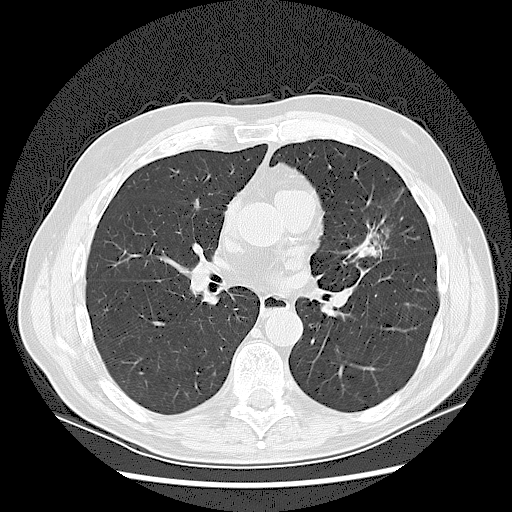
Low-dose screening chest CT, axial slice, baseline screening round, lung window (W 1500 / L -600 HU), lung (sharp) reconstruction kernel (LUNG), slice 65 of 132 in the series. Male participant, aged 65 years at enrolment. Current smoker at enrolment.
• Expert-annotated lung lesion, bounding box <344,216,400,265> (left, top, right, bottom; pixels).
• Screening reader's record for this exam (one nodule recorded; not confirmed to be the boxed lesion): non-calcified nodule or mass ≥4 mm, left upper lobe, 37 × 27 mm, spiculated (stellate) margins, soft tissue attenuation.
• Official screen result: positive, change unspecified: nodule(s) >= 4 mm or enlarging nodule(s), mass(es), or other non-specific abnormalities suspicious for lung cancer.
• Participant outcome: lung cancer diagnosed 56 days after this screen — non-small cell carcinoma, poorly differentiated (G3), stage IA (AJCC 6th edition).